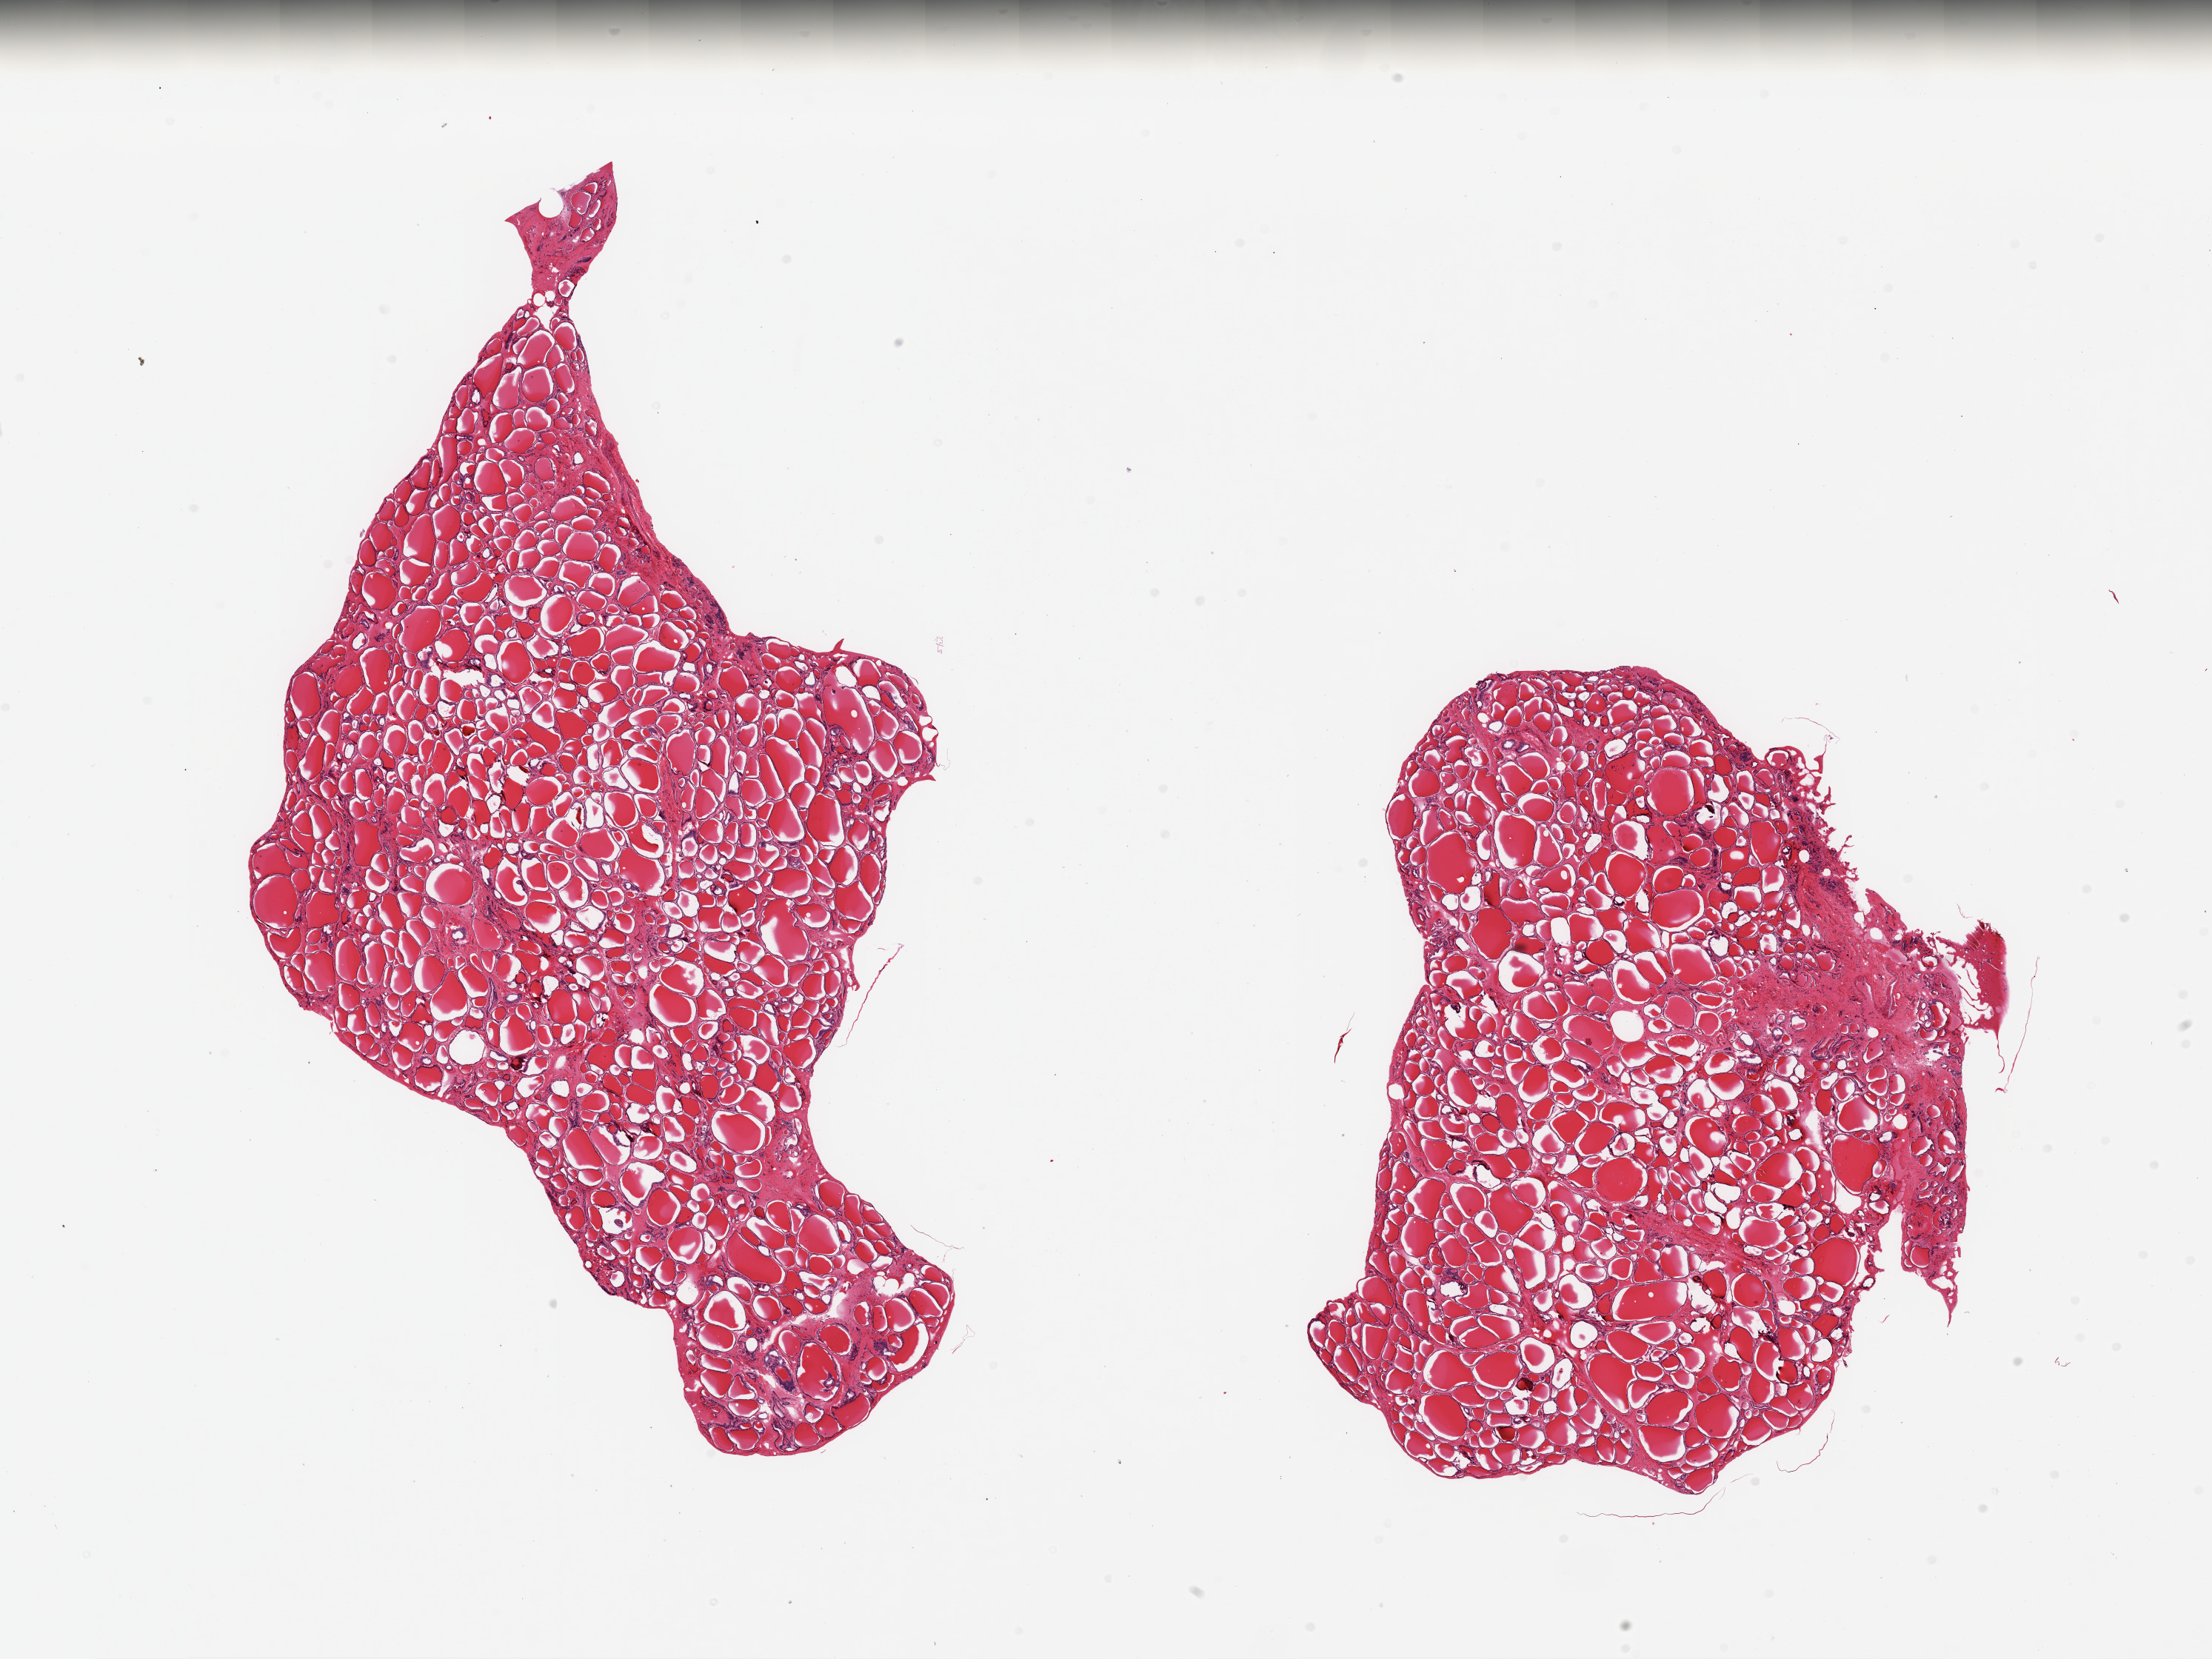
Hematoxylin and eosin (H&E) whole-slide image — whole scanned area (about 23.6 x 17.7 mm) shown as a low-resolution overview; PAXgene-fixed, paraffin-embedded tissue; sampled site (target tissue): thyroid; tissue donor sample. Male donor.
Reviewer comment on this tissue sample: 2 pieces; well trimmed; no lesions.